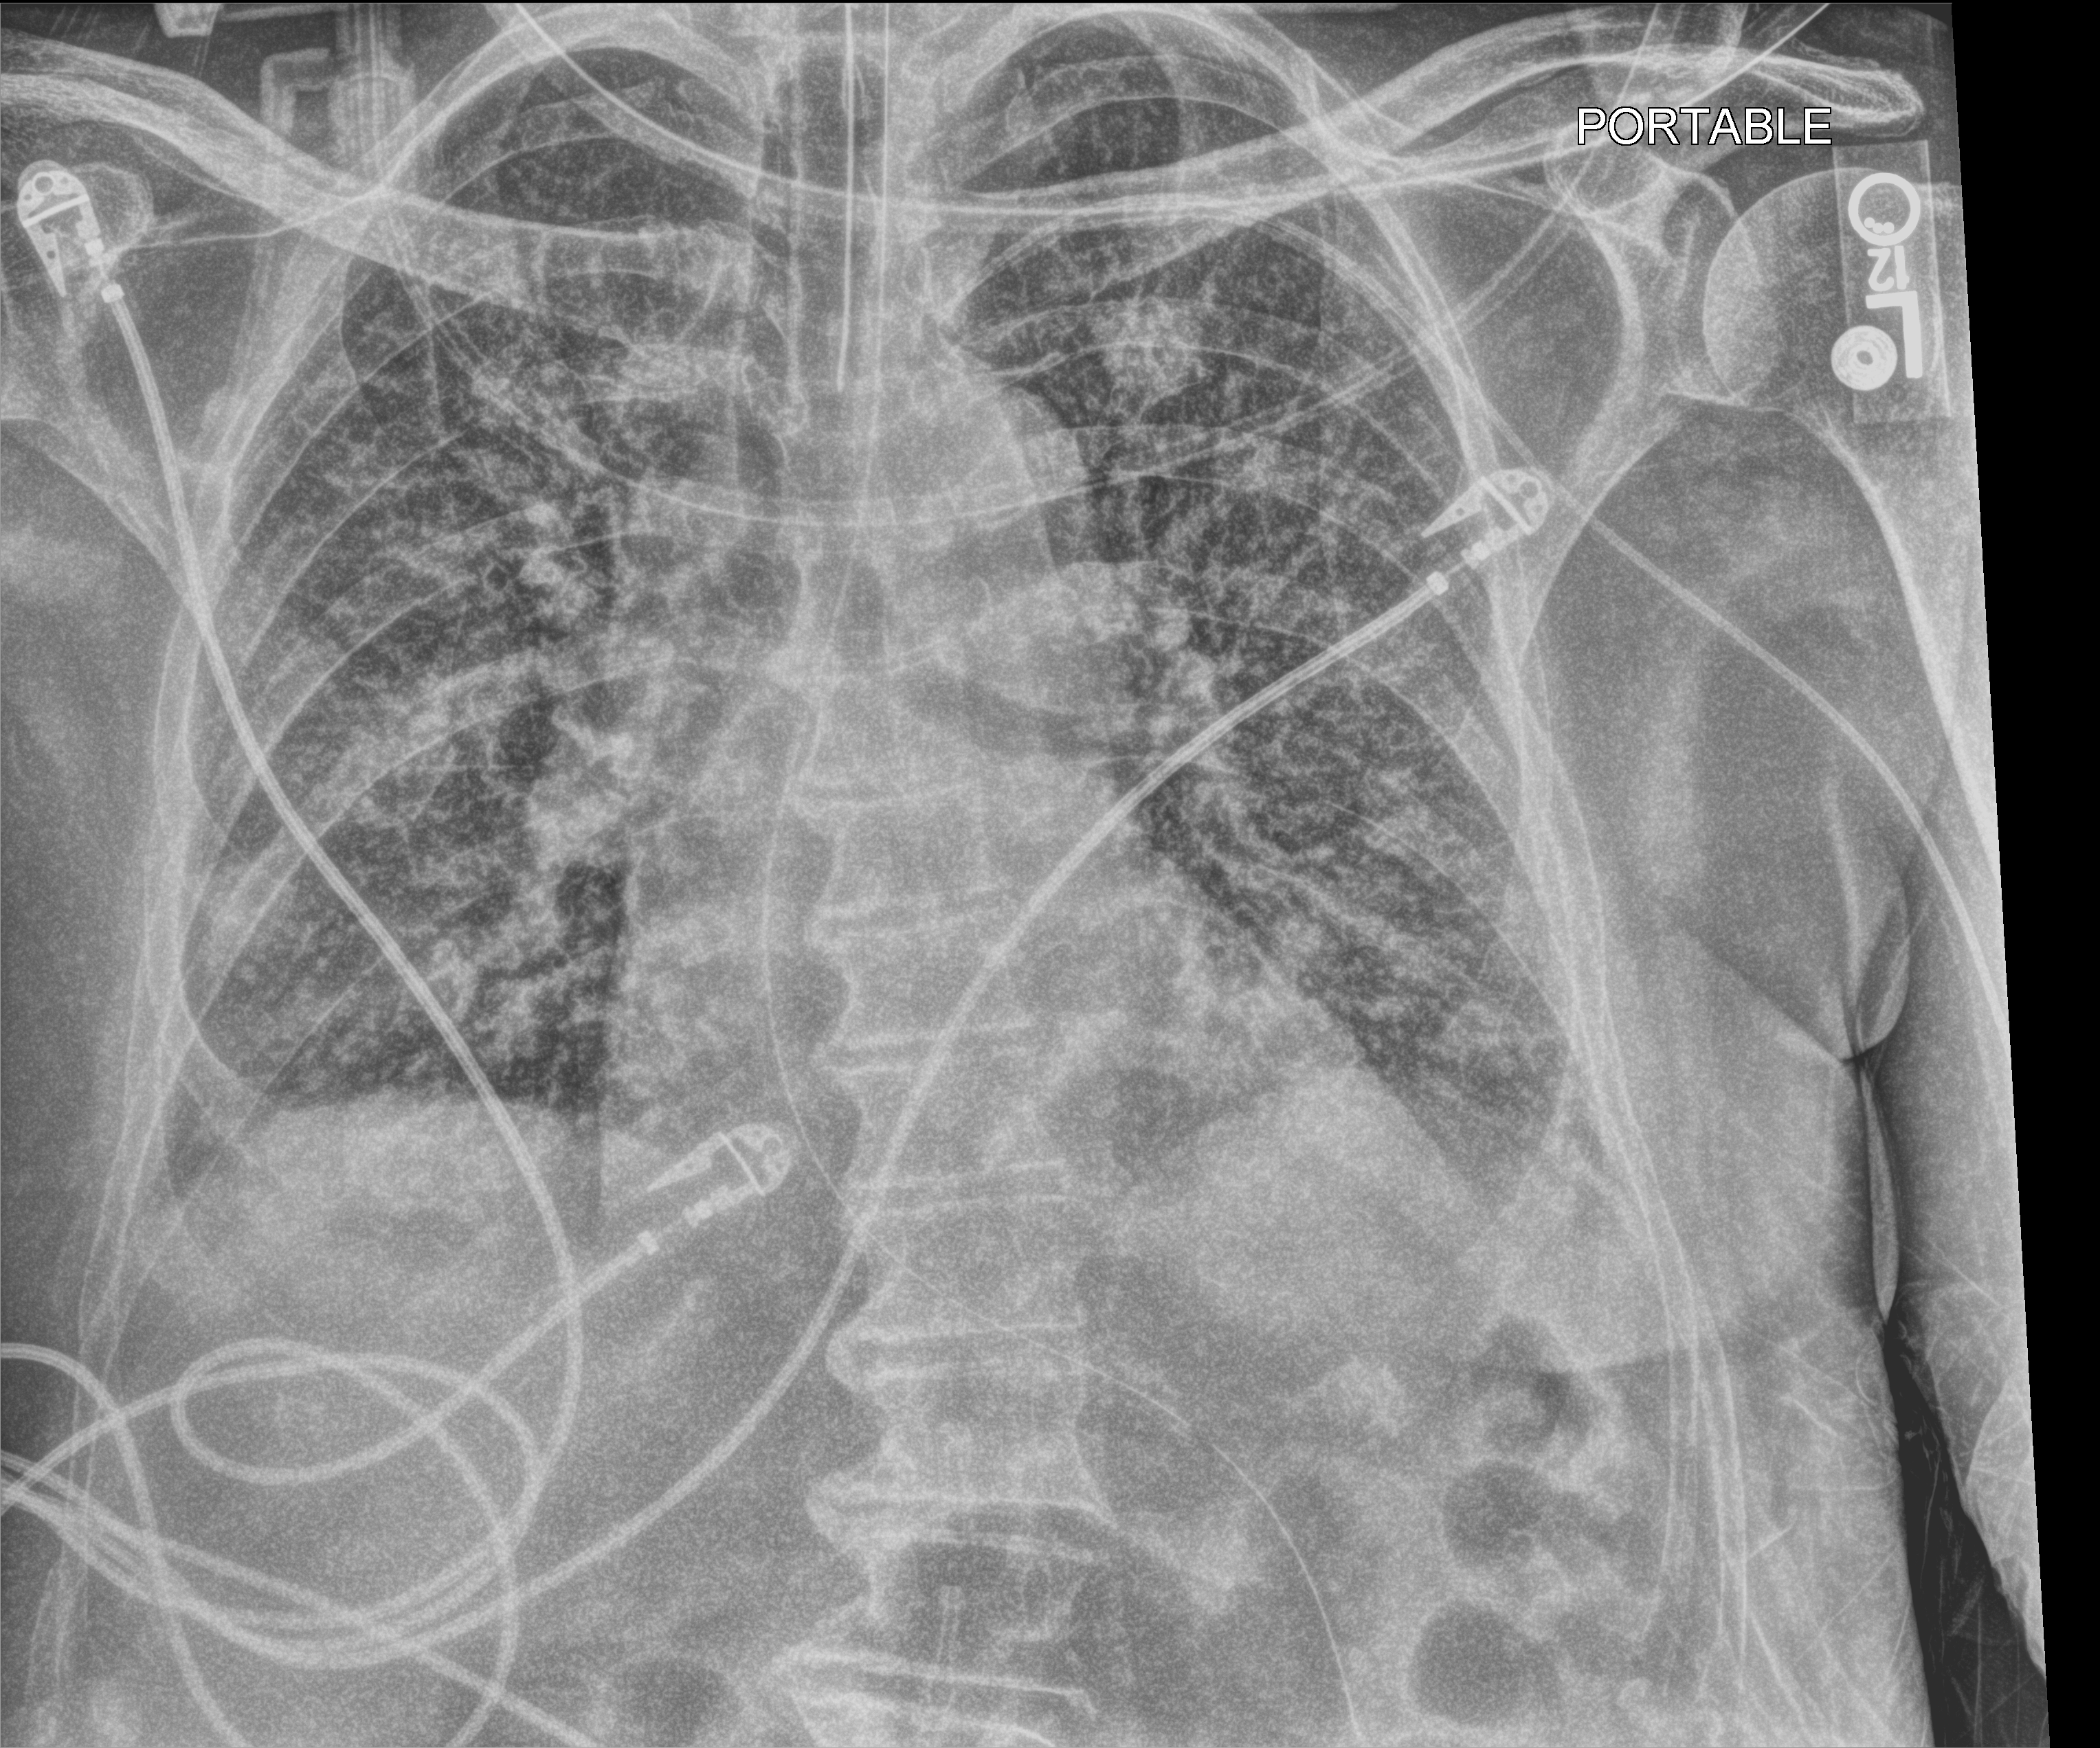
Portable chest radiograph. Male patient hospitalised with COVID-19, age 75–90 years.
Hospital-stay facts (about this admission, not read from this image; timing relative to this image not recorded): other chronic lung disease (admission record): no; admitted to intensive care during this hospital stay: yes.